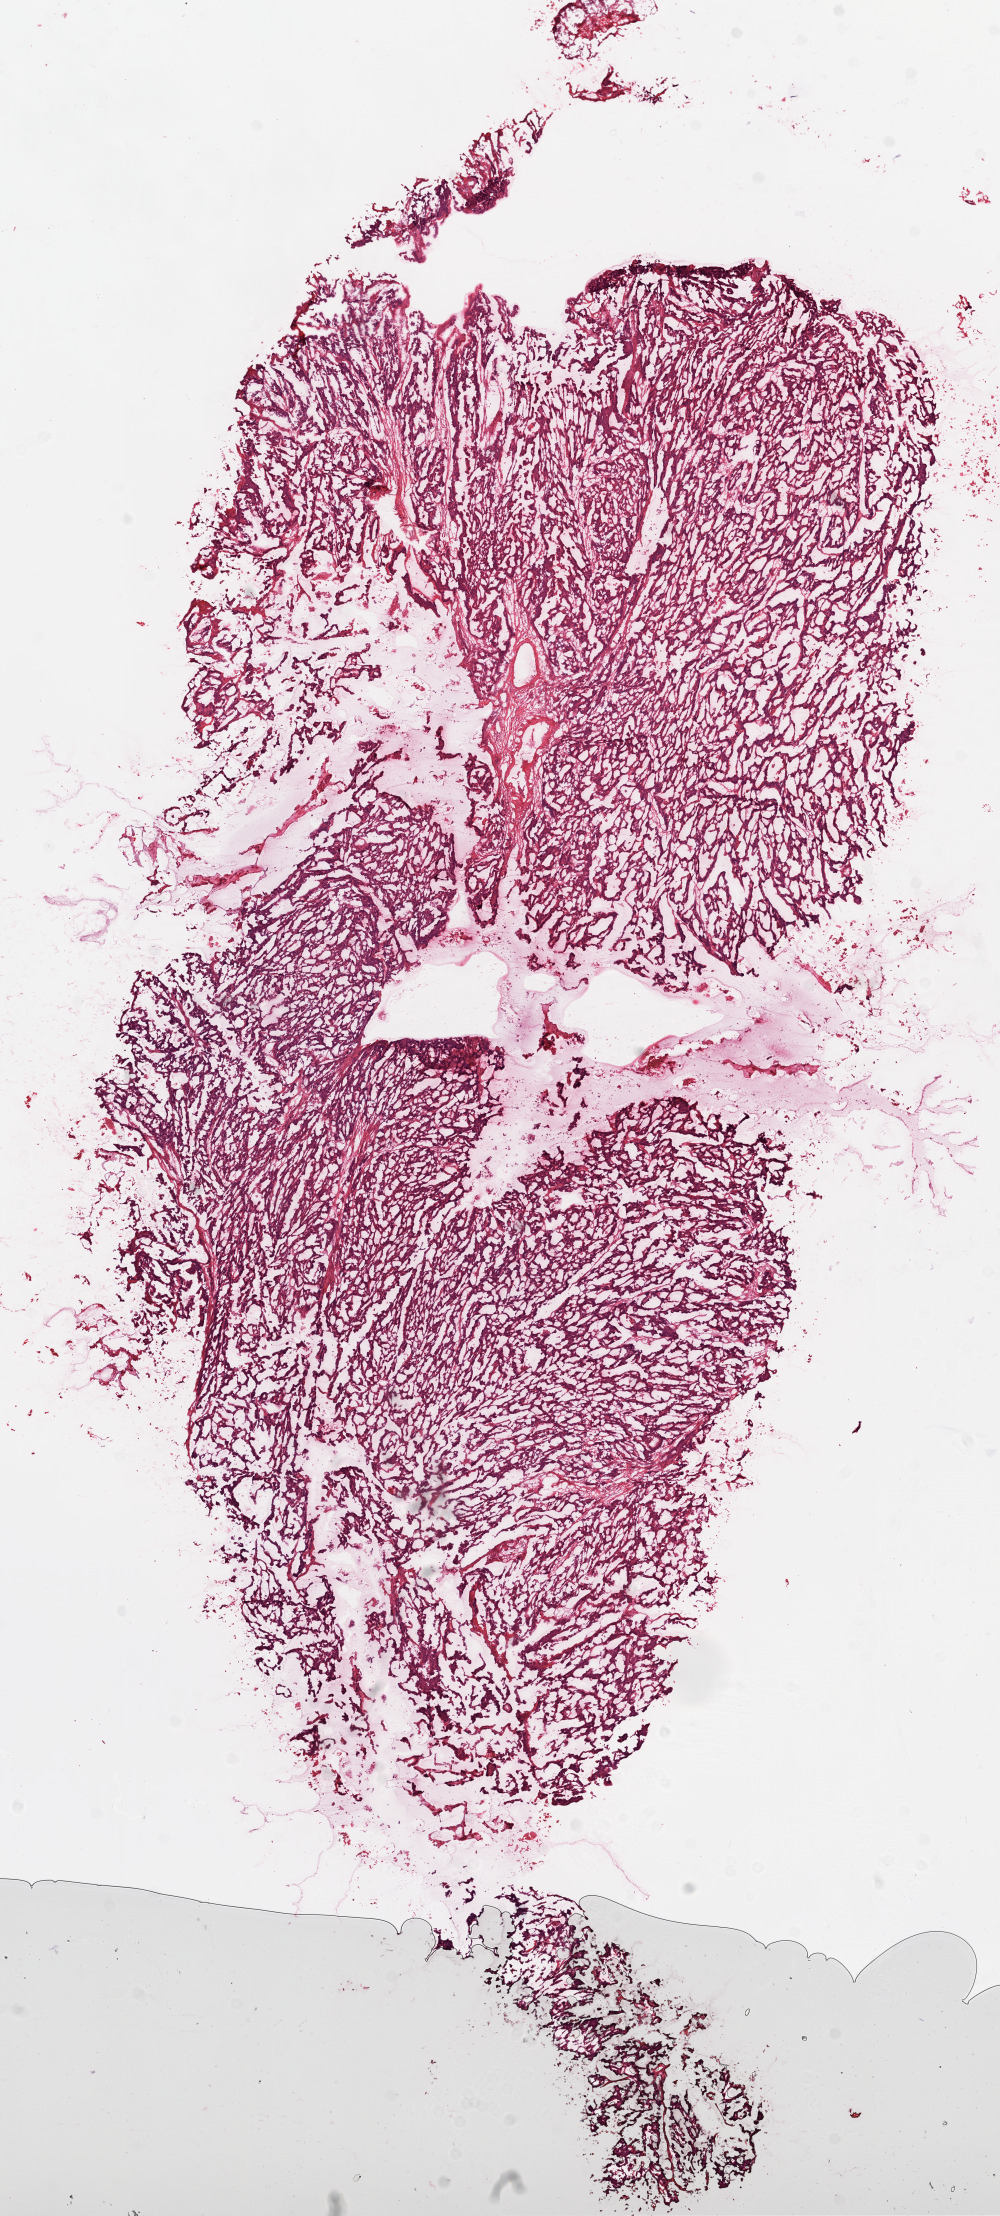
Digitized H&E-stained tissue section (whole slide) — a low-resolution overview of the entire scanned area, about 8.0 x 17.8 mm; frozen section from the top of the tissue portion; sample: primary tumour, colon. Female, age 71 years at initial diagnosis. Composition of this section per pathologist review: tumour cells 90%, tumour nuclei 80%, normal cells 0%, stromal cells 5%, necrosis 5%.
* AJCC pathologic stage: IVA
* histologic diagnosis: Adenocarcinoma, NOS (cecum)
* lymph nodes positive (case pathology): 2 of 4 examined